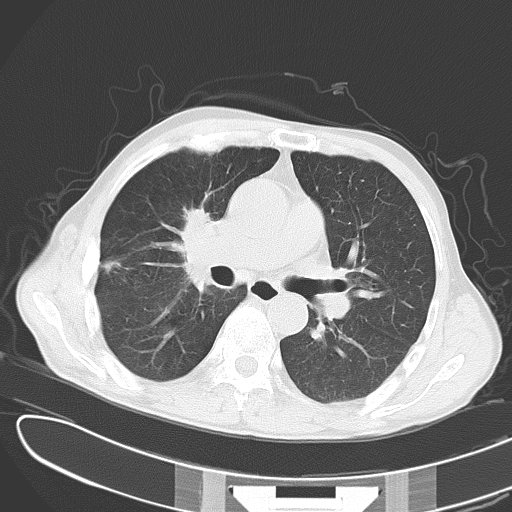
Chest CT, one axial slice; slice 20 of 43 in the series (ordered by position); 120 kVp; lung window (W 1500 / L -600 HU); 5 mm slice thickness; 512 × 512 image matrix, field of view 353 × 353 mm. Male patient, age 65 years. From the clinical record (not read from this slice): clinical TNM (as recorded): T2 N3 M1; histopathological grade: G3.
Annotated regions visible in this slice (rectangle marked by the reading radiologist):
- lung tumour (recorded histology: small cell carcinoma): bounding box <180,201,237,303> (left, top, right, bottom; pixels)